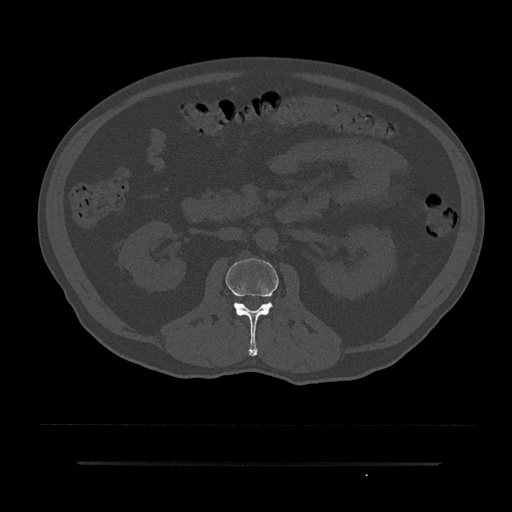
CT including the spine, one axial slice. Slice 68 of 797 in the series (ordered by position). Bone window (W 1800 / L 400 HU). 0.5 mm slice thickness. 512 × 512 image matrix, field of view 464 × 464 mm. Patient: male, 59 years. Case-level facts recorded for this patient, not image findings: primary cancer: bile ducts.
Structures marked on this image (semi-automatically segmented with operator editing):
- L2 vertebra: bounding box <226,258,279,356> (left, top, right, bottom; pixels)